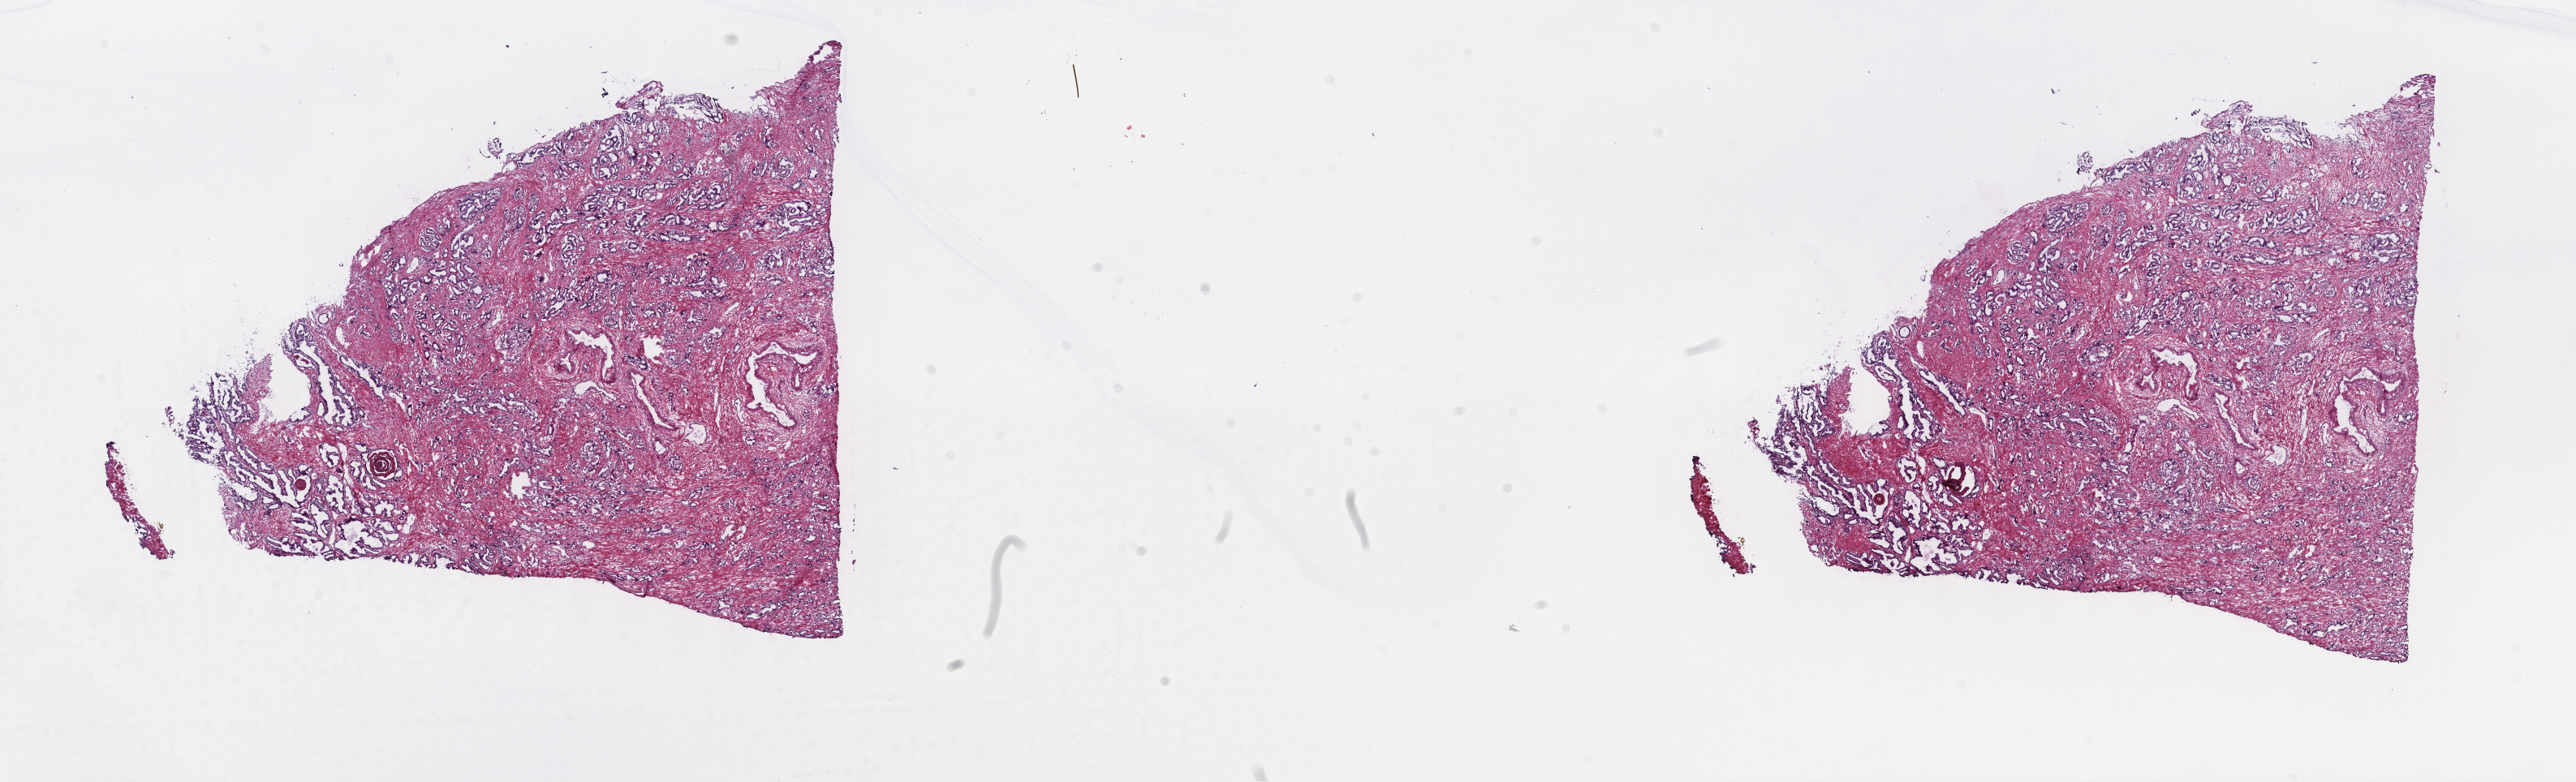
Digitized H&E-stained tissue section (whole slide), whole scanned area (about 25.7 x 7.8 mm, acquisition: 40x scan) shown as a low-resolution overview. Frozen section from the top of the tissue portion. Sample: primary tumour, prostate. Male, age 55 years at initial diagnosis. Gleason score: 7 (3+4). Slide review estimates, as recorded: tumour cells 85%, tumour nuclei 60%, normal cells 15%, stromal cells 0%, necrosis 0%. Infiltration values recorded for this section: lymphocyte infiltration 2%, monocyte infiltration 0%, neutrophil infiltration 0%.
Laterality: right. Diagnosis: Adenocarcinoma, NOS (prostate gland).